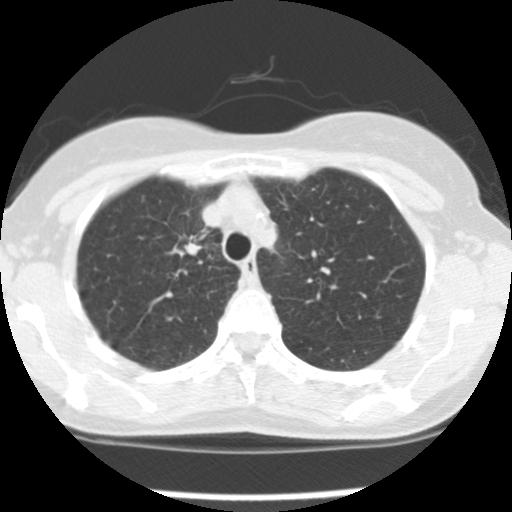
Axial slice from a low-dose chest CT screening exam, baseline screening round, lung window (W 1500 / L -600 HU), 2.5 mm slice thickness, standard (soft-tissue) reconstruction kernel (STANDARD). Female participant, aged 57 years at enrolment. Current smoker at enrolment.
Expert-annotated lung lesion, box from (x=165, y=227) to (x=218, y=275) px. Screening reader's record for this exam (one nodule recorded; not confirmed to be the boxed lesion): non-calcified nodule or mass ≥4 mm, left upper lobe, 7 × 6 mm, poorly defined margins, ground glass attenuation. Note: the box lies in the patient's right hemithorax on this image, whereas the reader's record names the left lung; they may be different findings. Participant outcome: lung cancer diagnosed 15 days after this screen — adenocarcinoma, NOS, right upper lobe, moderately differentiated (G2), stage IA (AJCC 6th edition), 15 mm at pathology.